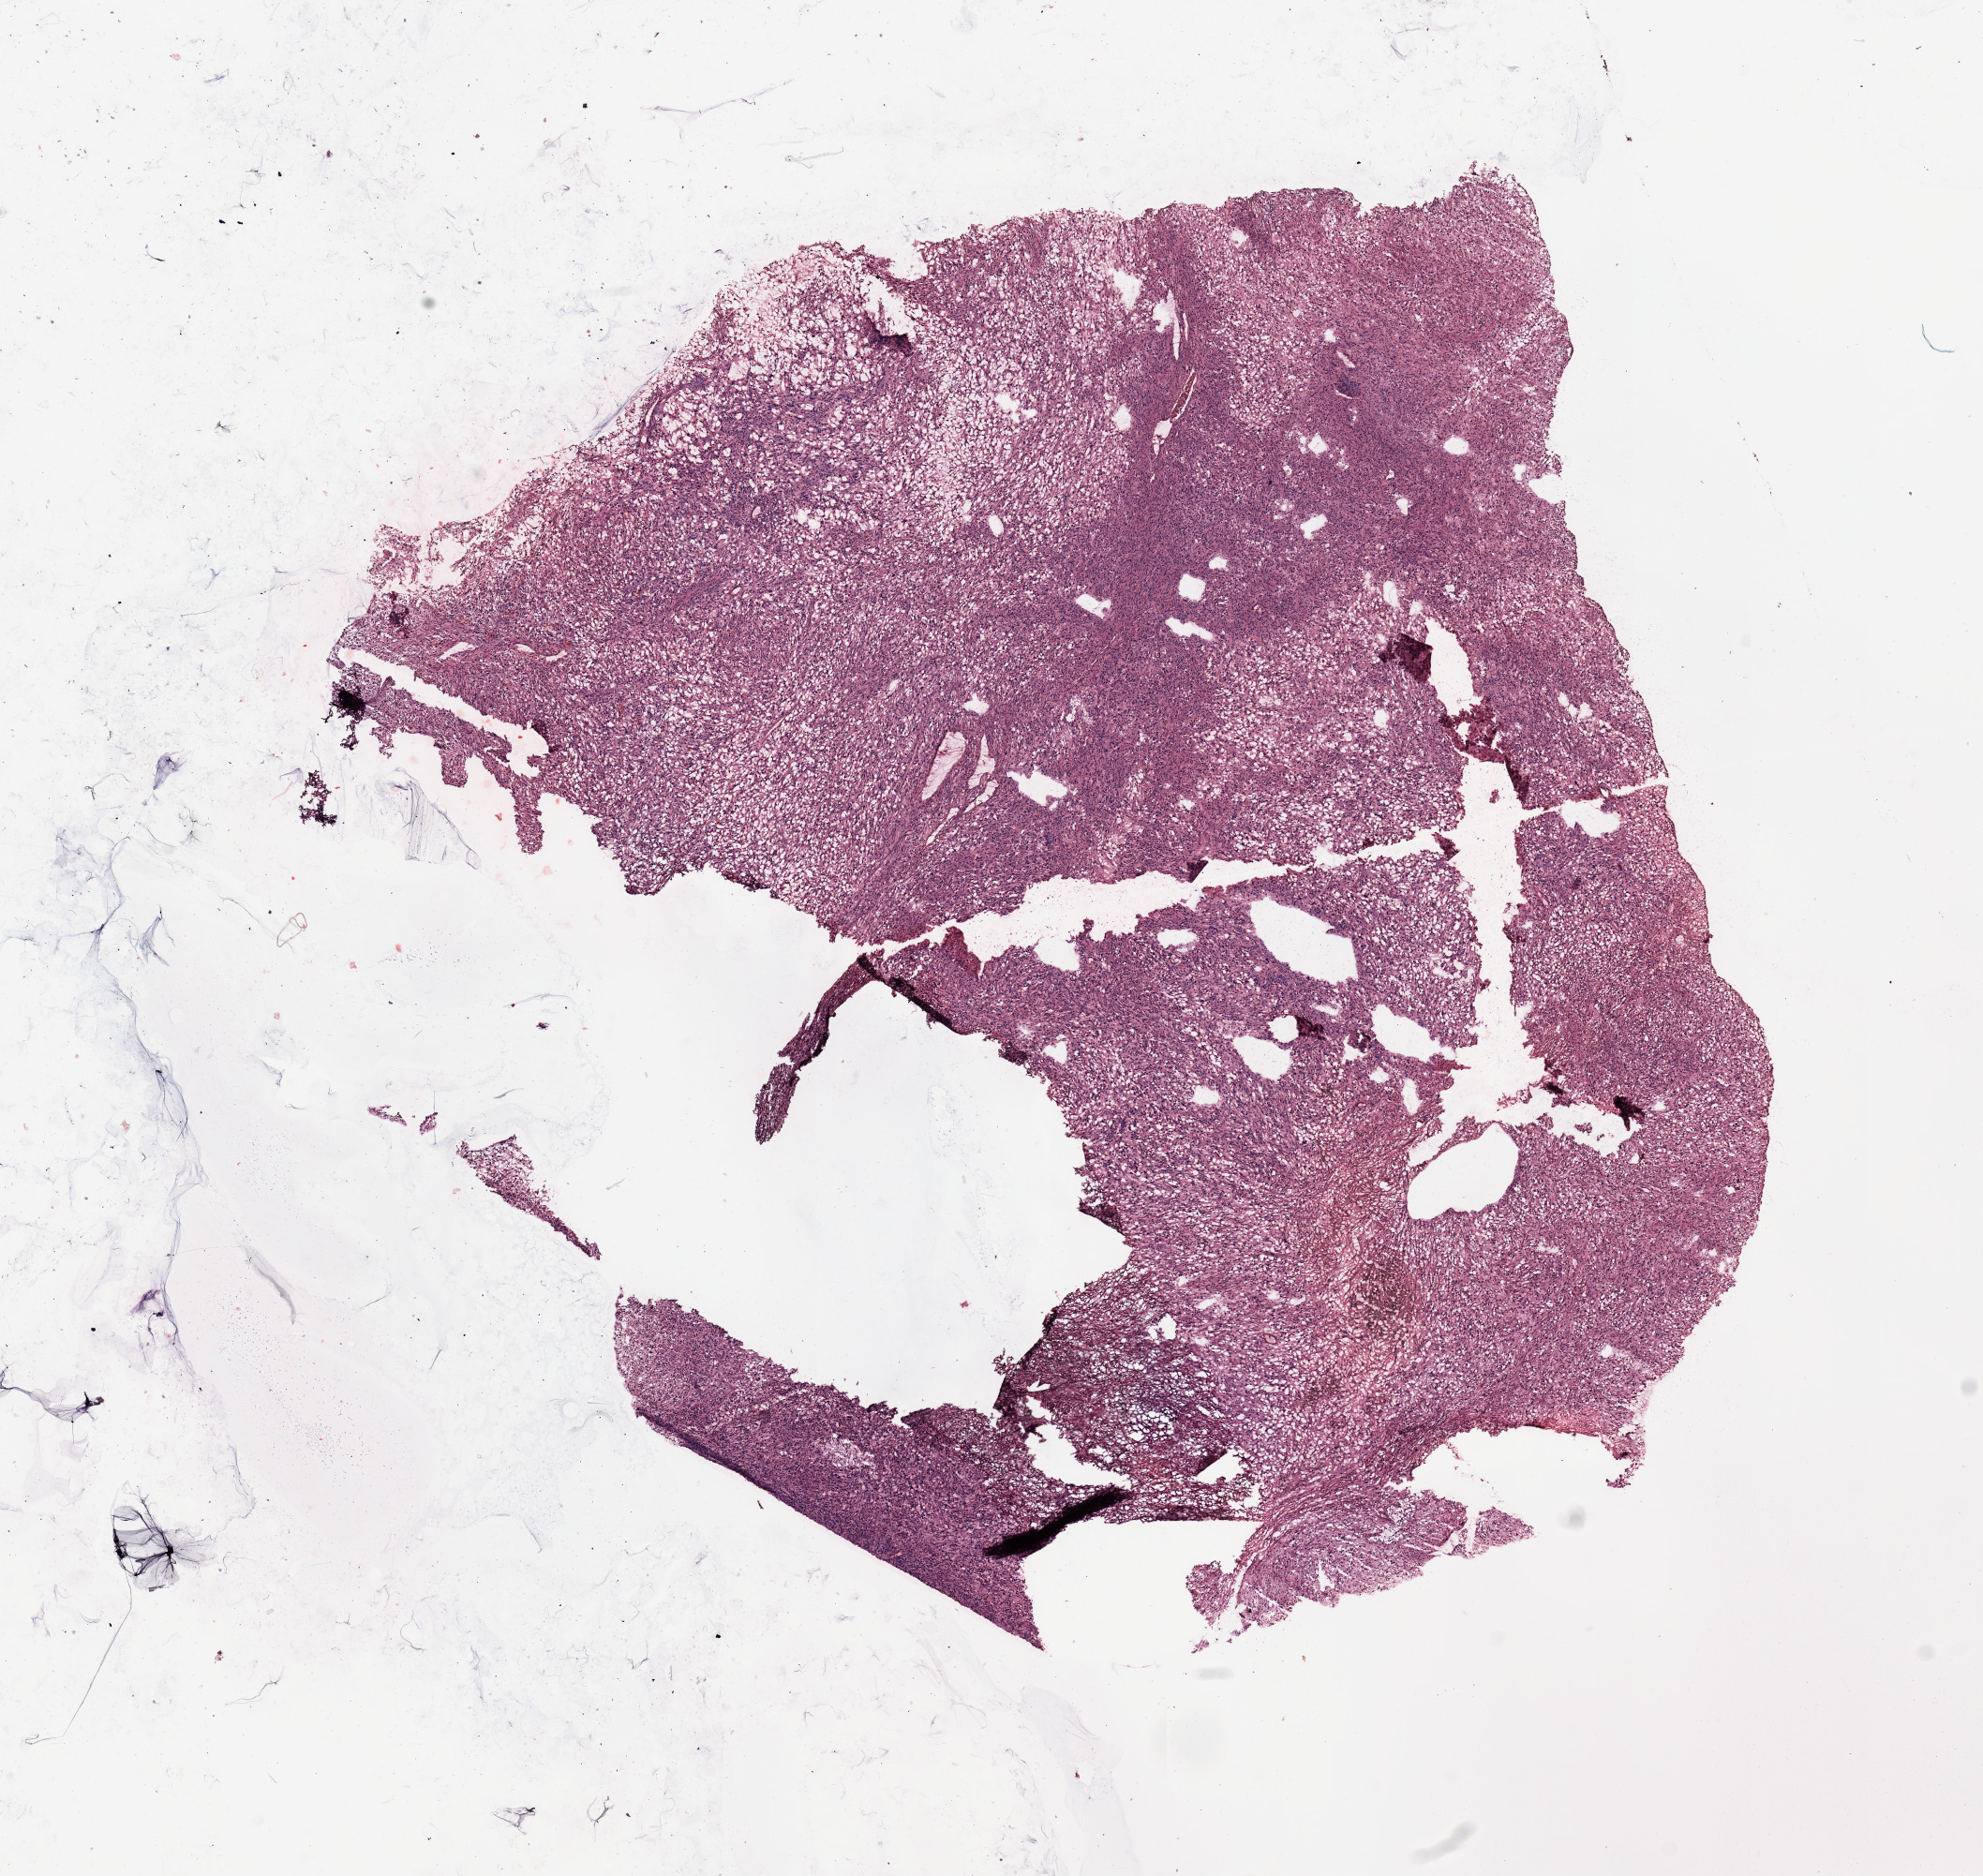
Whole-slide histology image, H&E — shown as a low-resolution overview of the whole scanned area (about 16.7 x 15.8 mm). Tumour tissue sample. Male, 74 y/o.
Patient diagnosis (cohort enrolment): sarcoma (site not recorded at cohort level). Primary tumour site (as recorded): lower extremity.